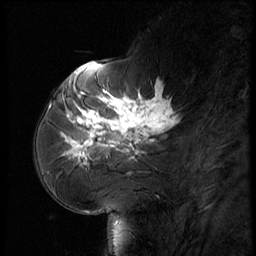
Breast MRI (dynamic contrast-enhanced), one sagittal slice. Slice 22 of 56 in the series (ordered by position). Dynamic contrast-enhanced series, image 2 of 3 at this slice position (ordered by acquisition). 1.5 T. TE 4.2 ms, TR 9 ms. 2.5 mm slice thickness. 256 × 256 image matrix. Female patient, age 61 years. From the clinical record (not read from this slice): setting: breast cancer imaged before/during neoadjuvant chemotherapy; receptor status: HR-positive, HER2-negative.
Annotated regions visible in this slice (semi-automatically segmented with operator editing):
- analysis volume of interest (the breast-tissue region the enhancement analysis was run in; not a lesion): bounding box <65,74,185,175> (left, top, right, bottom; pixels)
- tumour enhancement mask (voxels above the 140 % enhancement threshold inside the analysis volume of interest): <67,84,174,165>